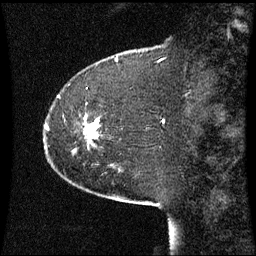
Breast MRI (dynamic contrast-enhanced), one sagittal slice; slice 14 of 60 in the series (ordered by position); dynamic contrast-enhanced series, image 2 of 3 at this slice position (ordered by acquisition); 1.5 T; TE 4.2 ms, TR 8.9 ms; 2.2 mm slice thickness; 256 × 256 image matrix, field of view 220 × 220 mm. Patient: female, 51 years. Case-level facts recorded for this patient, not image findings: setting: breast cancer imaged before/during neoadjuvant chemotherapy; receptor status: HR-positive, HER2-negative.
Structures marked on this image (semi-automatic segmentation, software-assisted and operator-edited):
- analysis volume of interest (the breast-tissue region the enhancement analysis was run in; not a lesion): bounding box <46,118,99,147> (left, top, right, bottom; pixels)
- tumour enhancement mask (voxels above the 70 % enhancement threshold inside the analysis volume of interest): <86,120,99,139>